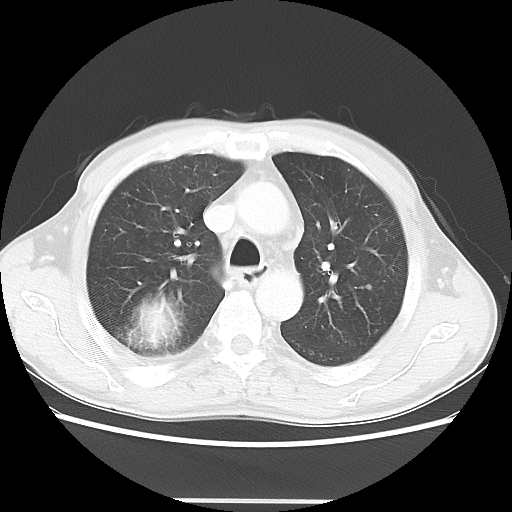
Chest CT, one axial slice. Position 36 of 48 along the scan axis. Lung window (W 1500 / L -600 HU). 512 × 512 image matrix, field of view 361 × 361 mm. Patient: male, 66 years. Case-level facts recorded for this patient, not image findings: clinical TNM (as recorded): T4 N1 M1; histopathological grade: G3.
Structures marked on this image (rectangle marked by the reading radiologist):
- lung tumour (recorded histology: small cell carcinoma): bounding box <115,291,201,366> (left, top, right, bottom; pixels)